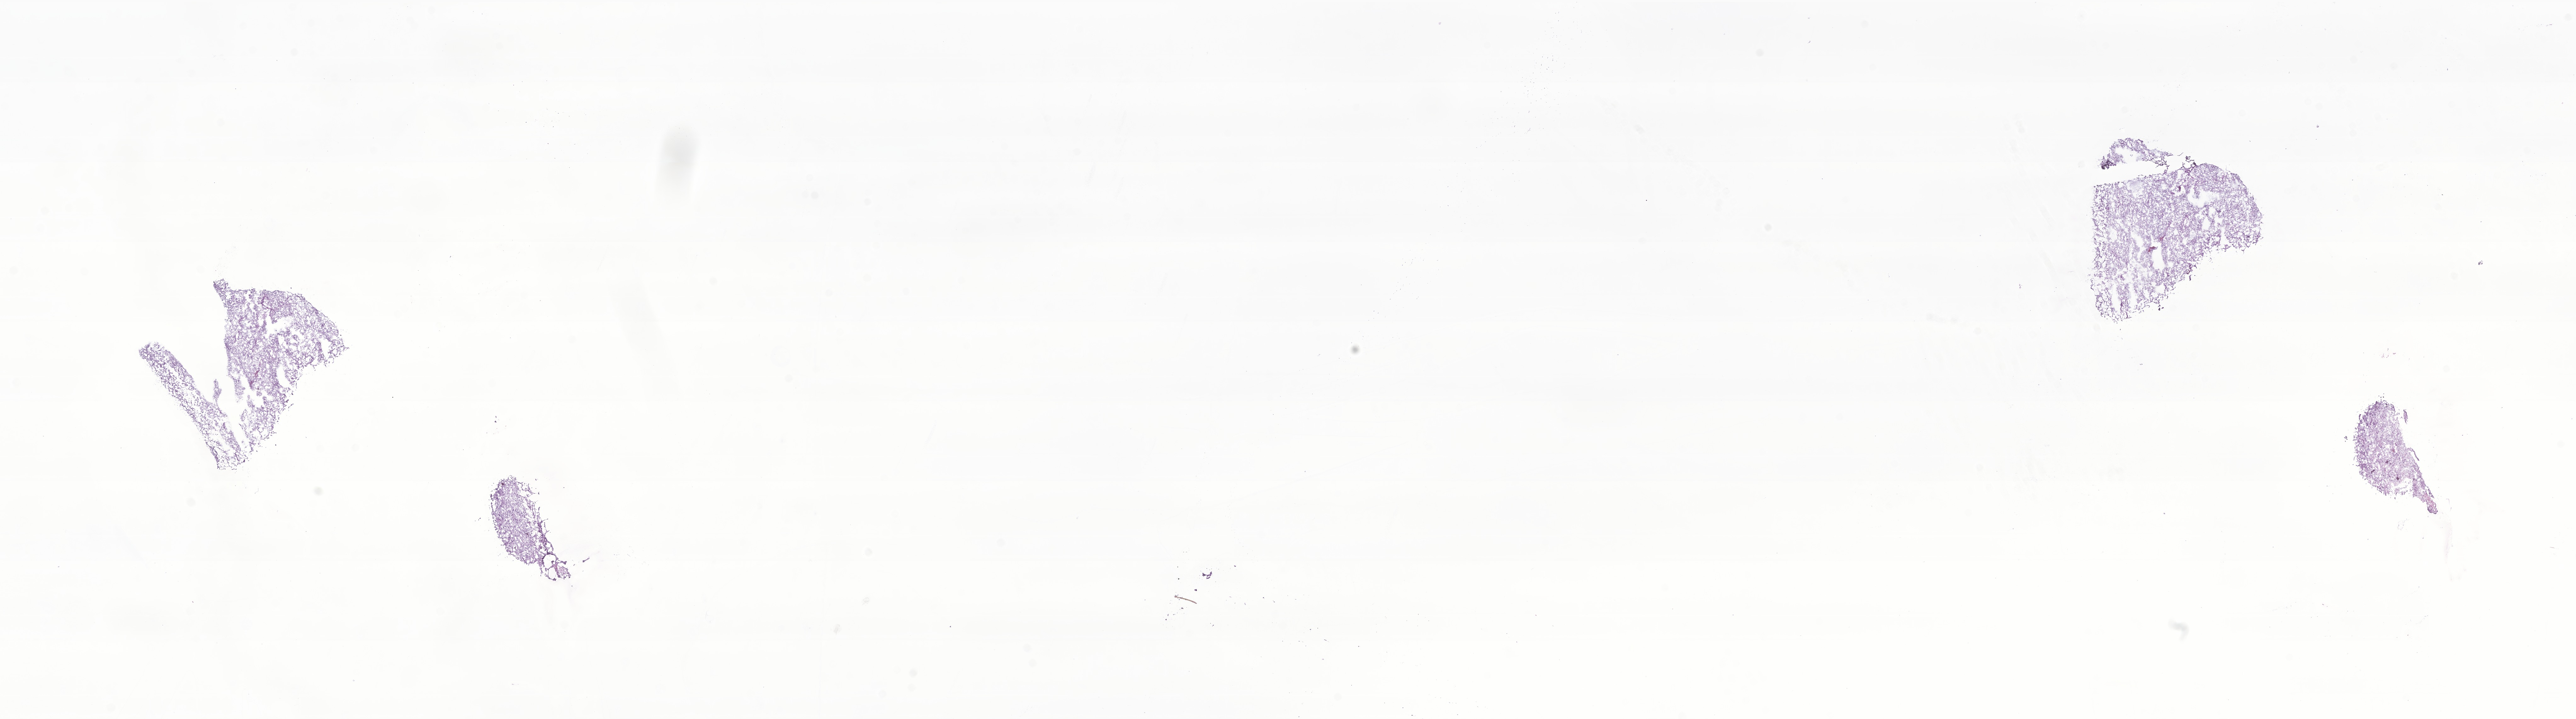
Whole-slide image, H&E stain of tumor tissue from the brain — shown as a low-resolution overview of the whole scanned area (about 34.5 x 9.6 mm); cryosection (OCT / tissue freezing medium). Patient female; age 138 months.
Diagnosis: Glioma, malignant.